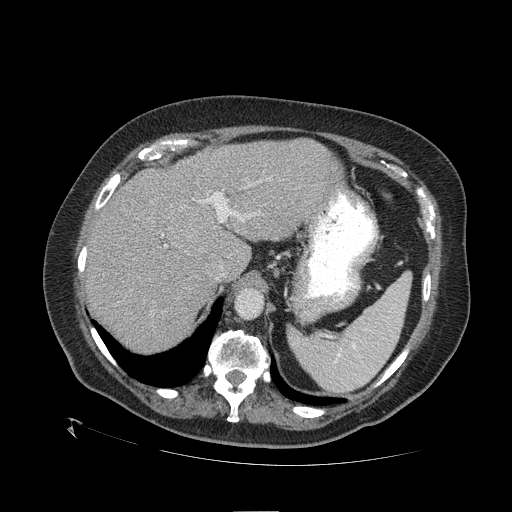
Contrast-enhanced abdominal CT (liver protocol), one axial slice; slice 79 of 109 in the series (ordered by position); 120 kVp; one of 2 acquisitions stored at this slice position; soft-tissue window (W 400 / L 40 HU); 2.5 mm slice thickness; 512 × 512 image matrix, field of view 460 × 460 mm. From the clinical record (not read from this slice): diagnosis: hepatocellular carcinoma (patient treated with transarterial chemoembolisation; whether this scan precedes or follows treatment is not stated here); TNM stage (as recorded): Stage-I; Child-Pugh class: A; tumour differentiation: no biopsy; tumour nodularity: uninodular.
Structures marked on this image (semi-automatic segmentation, software-assisted and operator-edited):
- liver parenchyma outside the tumour (the mass and vessels are separate outlines, so this box may not span the whole liver): box from (x=84, y=138) to (x=342, y=352) px
- mass: (x=167, y=202)–(x=216, y=256)
- liver vessels: (x=165, y=180)–(x=261, y=246)